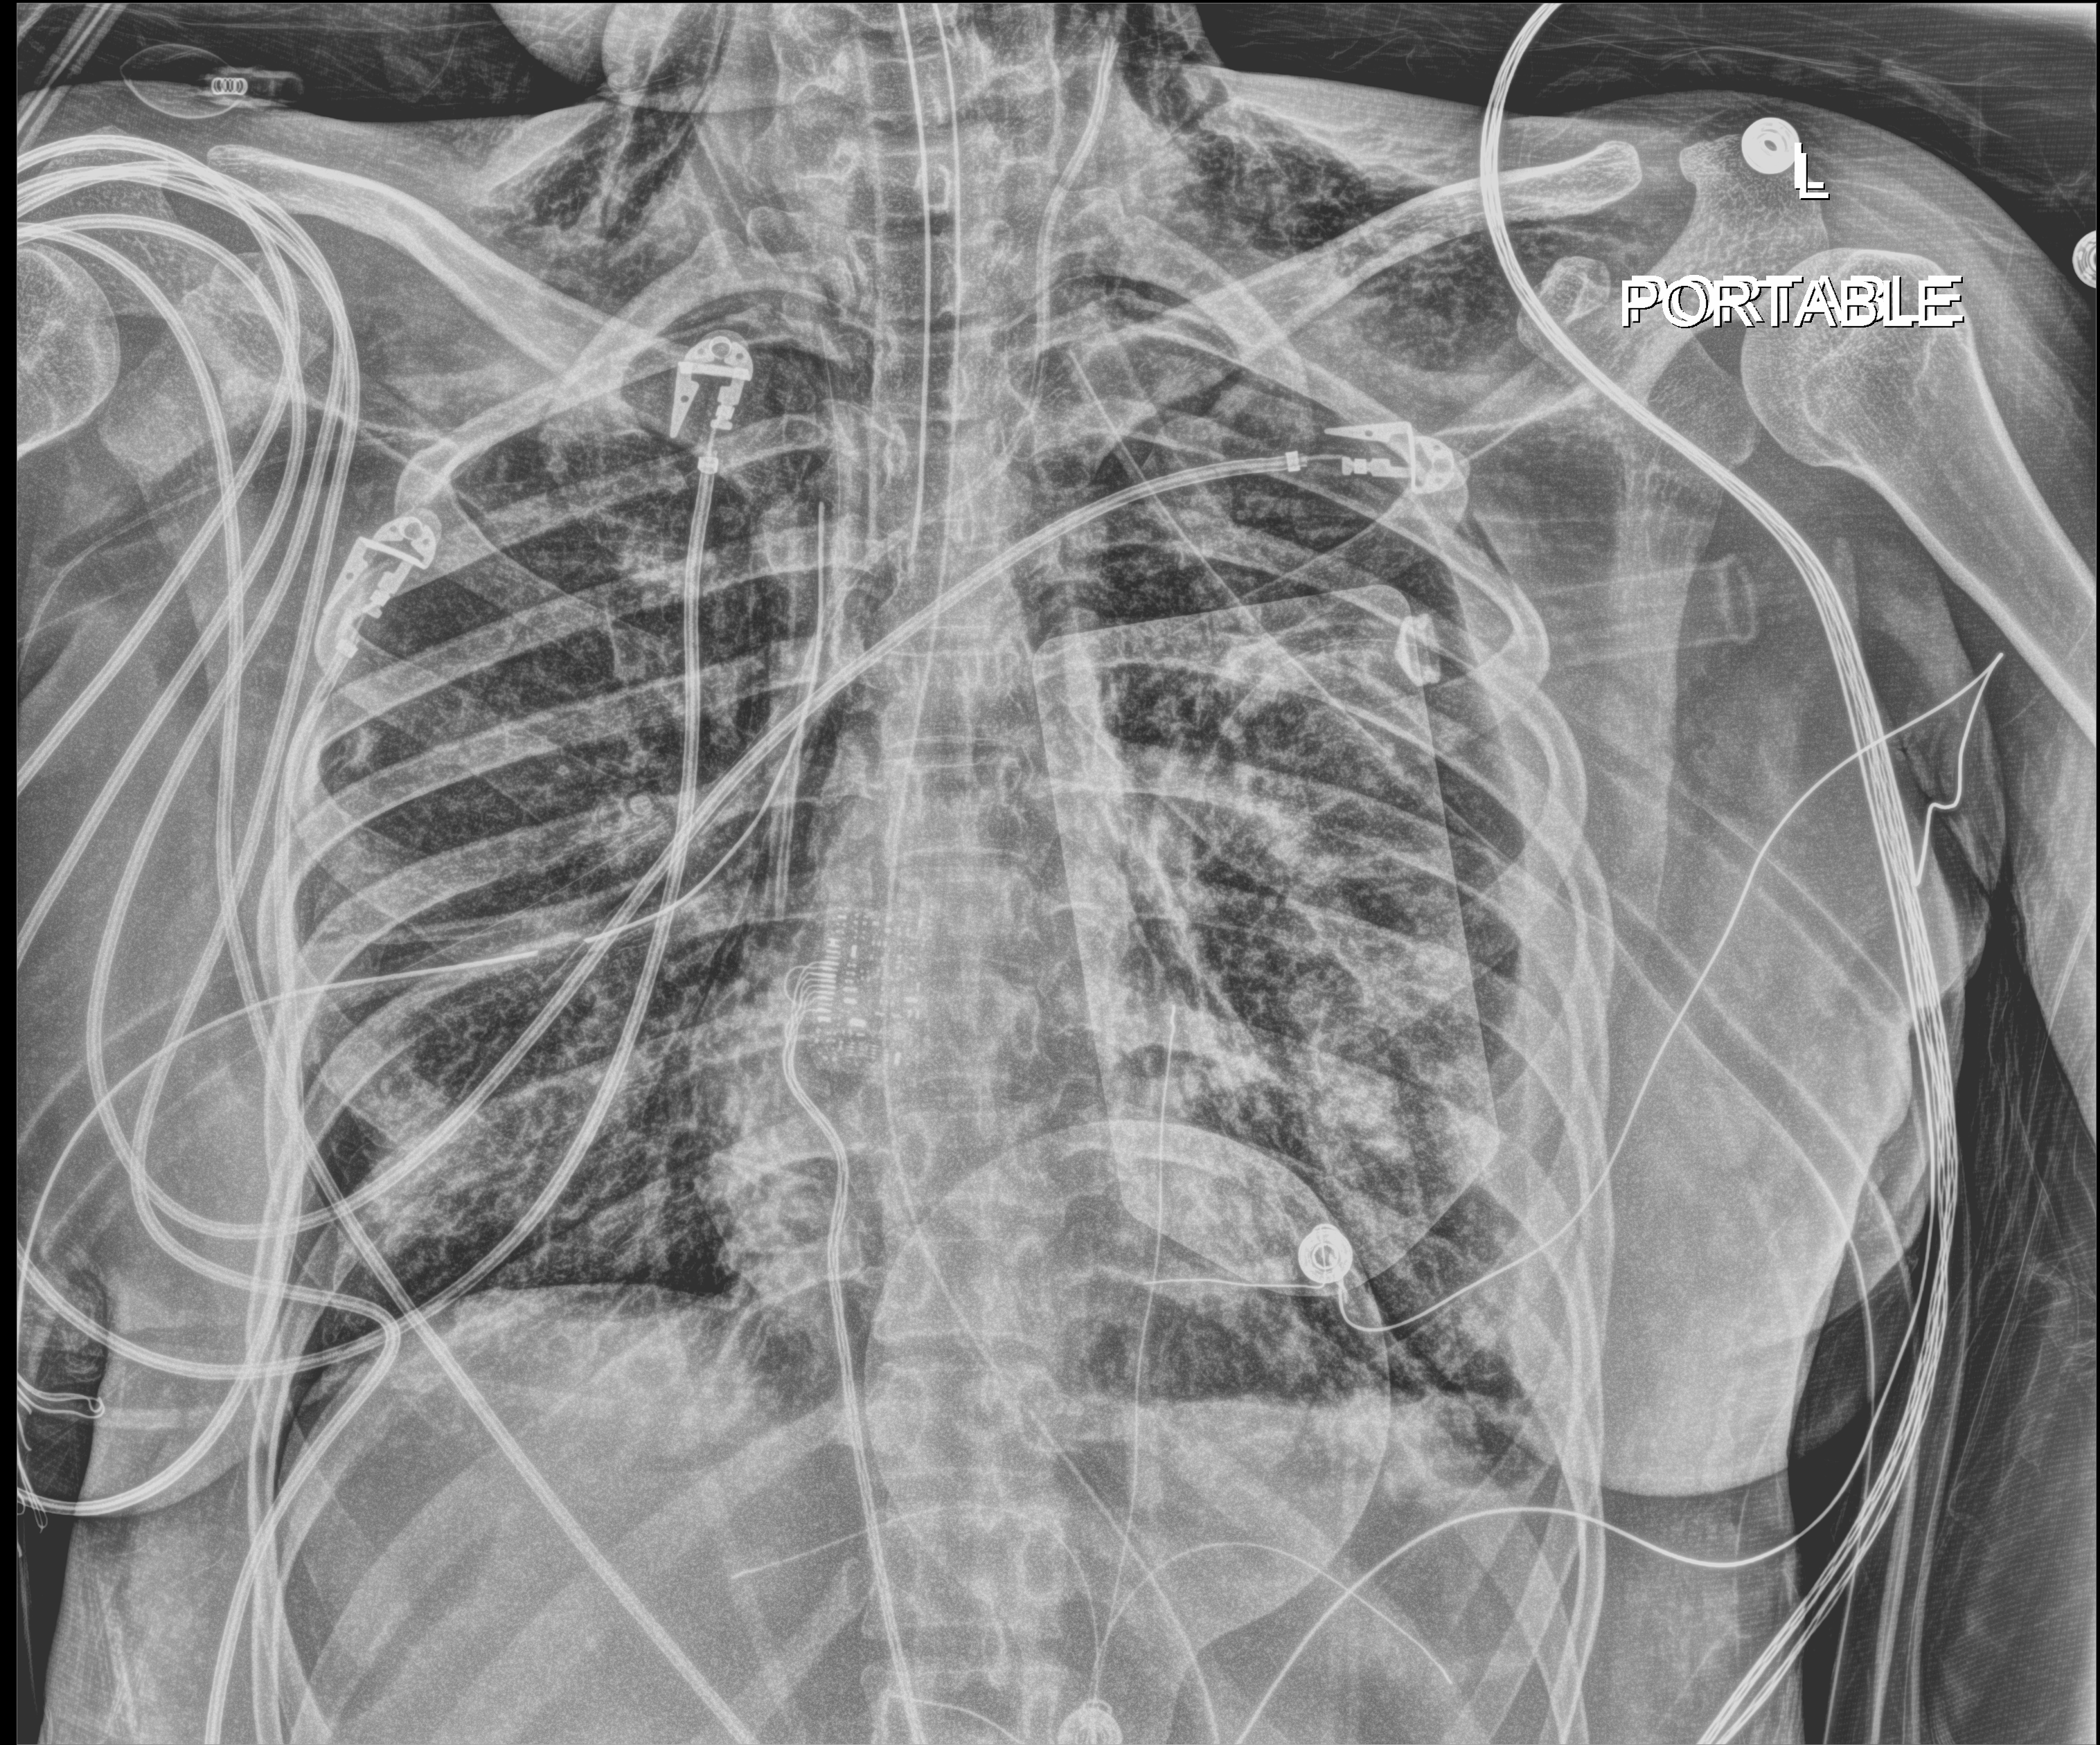
Chest X-ray (portable); anteroposterior (AP) projection. Adult patient hospitalised with COVID-19, age 18–59 years.
Admission-level facts for this patient (not findings on this image; timing relative to this image not recorded): mechanically ventilated during this hospital stay: yes.